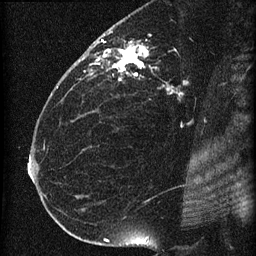
Breast MRI (dynamic contrast-enhanced), one sagittal slice. Position 38 of 60 along the scan axis. Dynamic contrast-enhanced series, image 2 of 4 at this slice position (ordered by acquisition). 1.5 T. TE 4.2 ms, TR 22.7 ms. 1.5 mm slice thickness. 256 × 256 image matrix, field of view 180 × 180 mm. Patient: female, 35 years. Case-level facts recorded for this patient, not image findings: setting: breast cancer imaged before/during neoadjuvant chemotherapy; receptor status: HR-positive, HER2-negative.
Structures marked on this image (semi-automatic segmentation, software-assisted and operator-edited):
- analysis volume of interest (the breast-tissue region the enhancement analysis was run in; not a lesion): bounding box (x1, y1, x2, y2) in pixels: (69, 27, 199, 112)
- tumour enhancement mask (voxels above the 90 % enhancement threshold inside the analysis volume of interest): (90, 39, 172, 93)